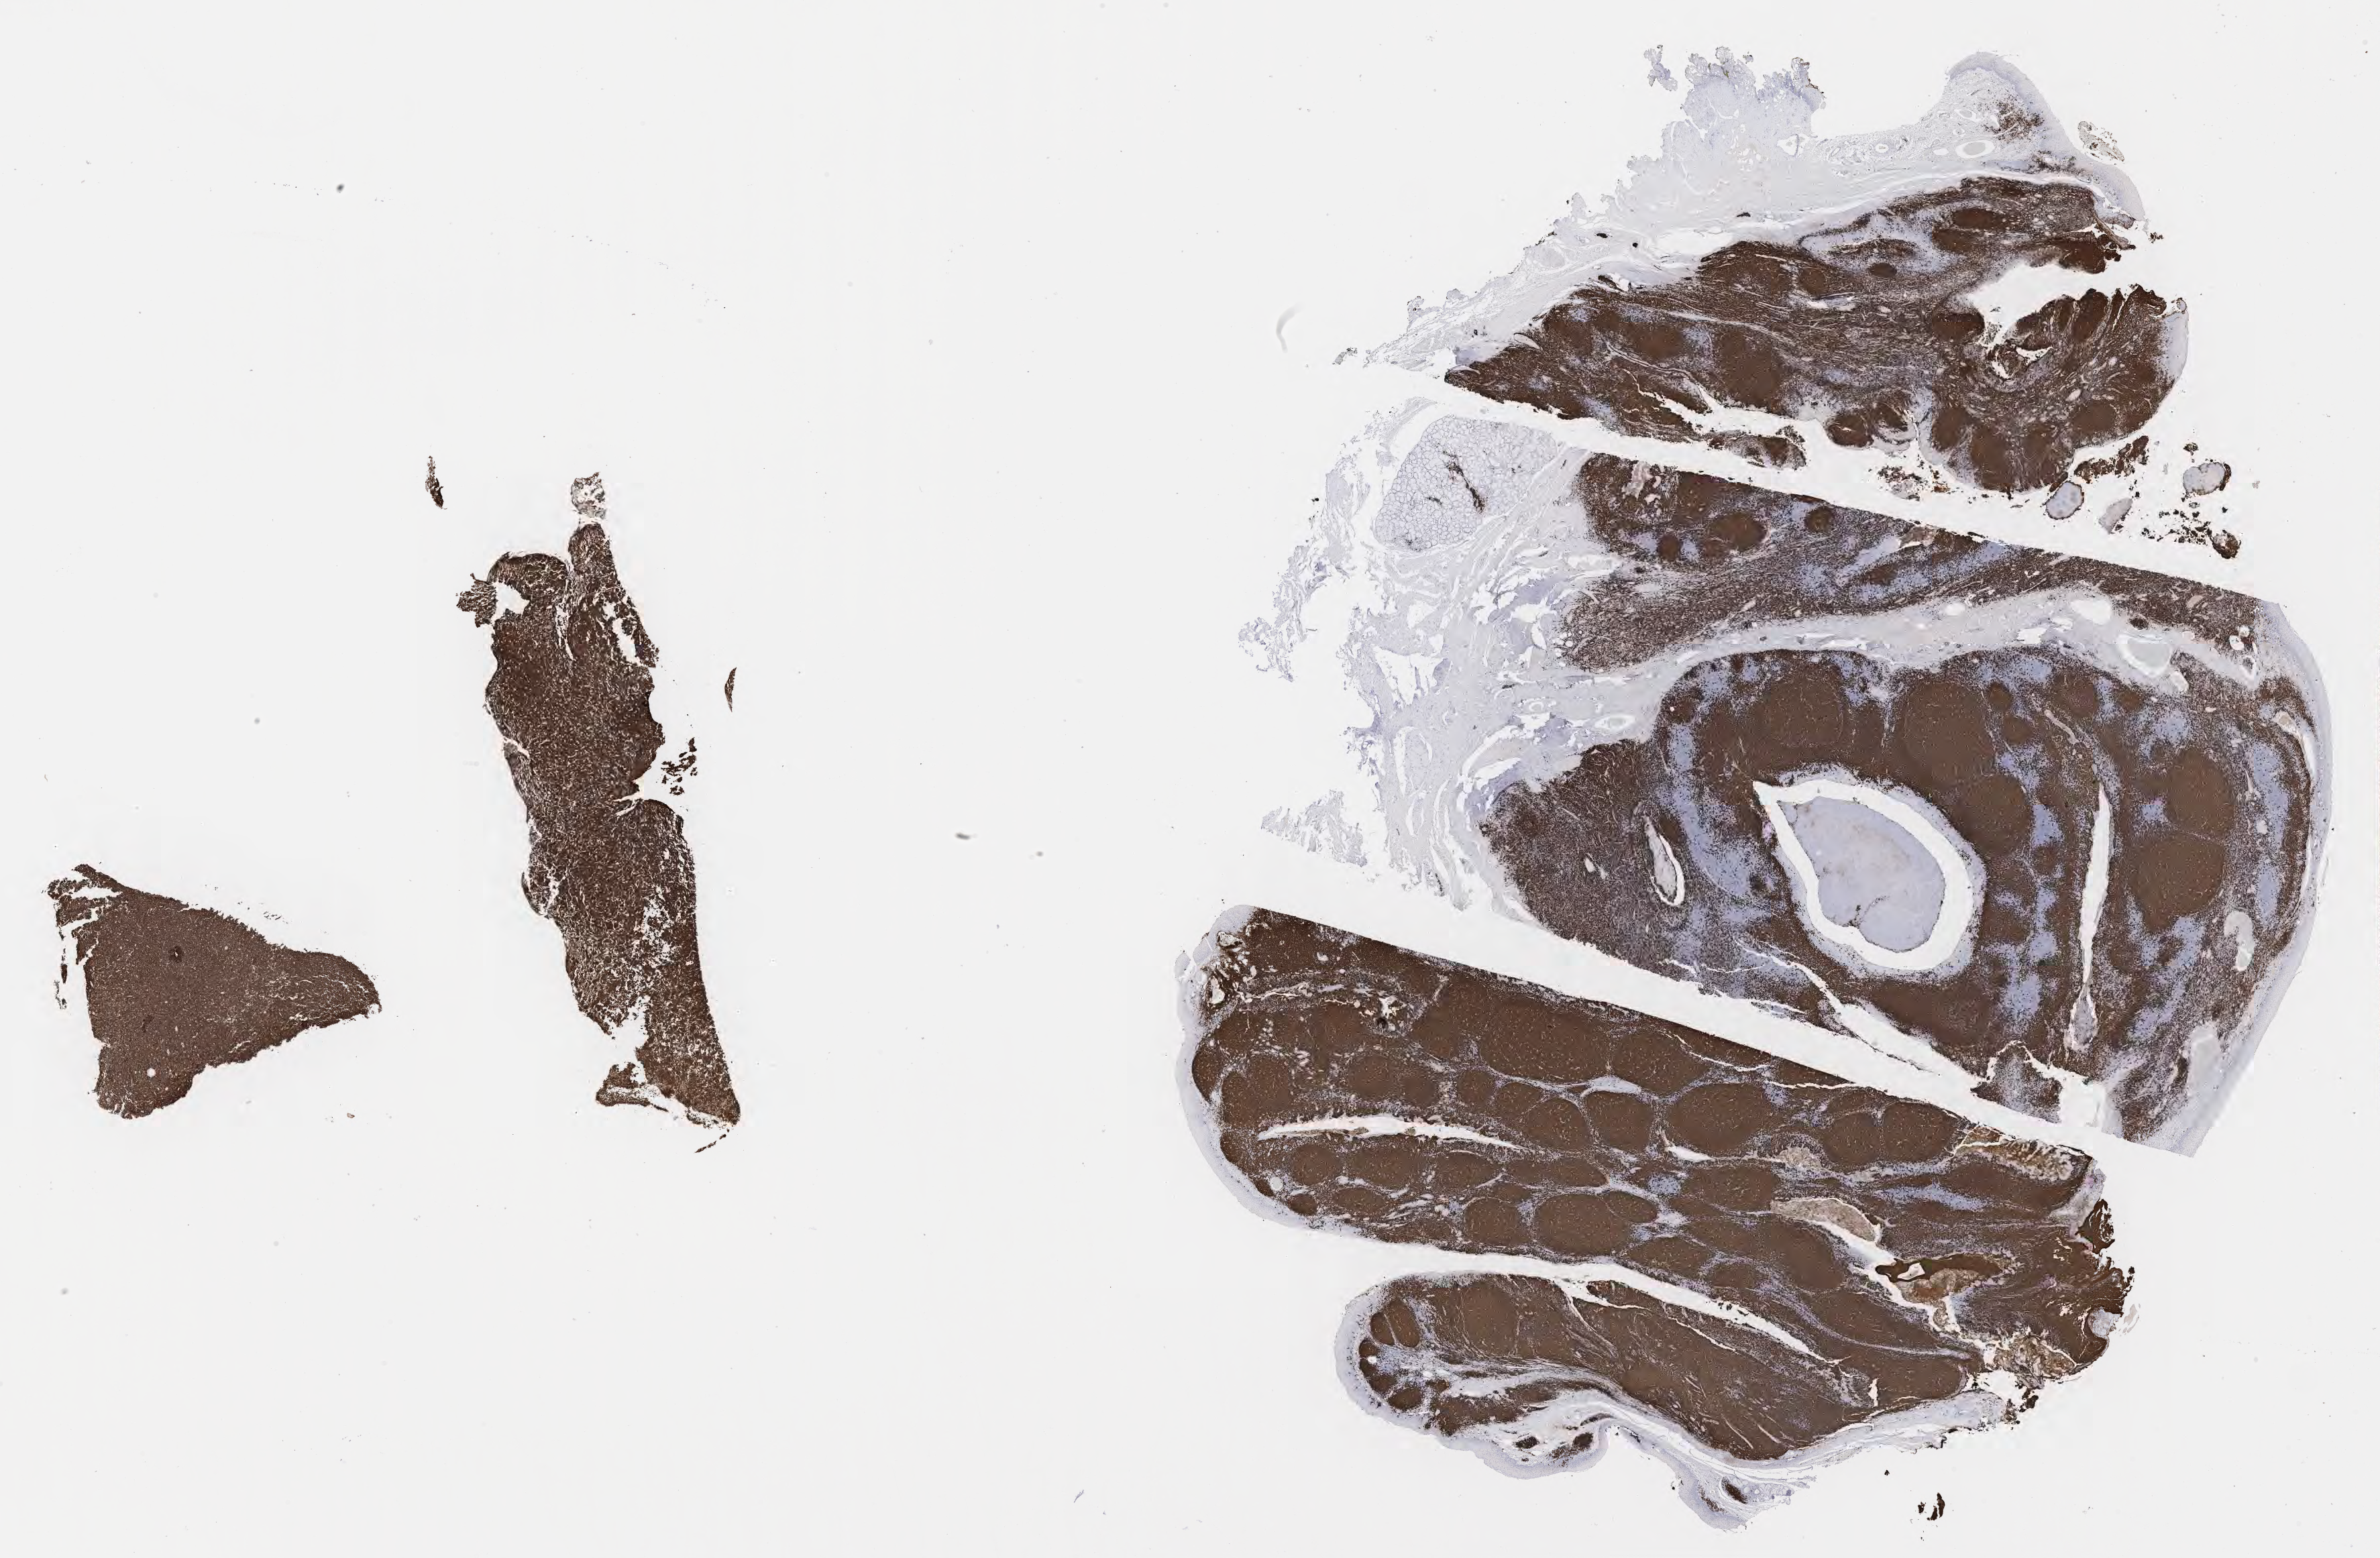
Whole-slide image, immunohistochemical stain for CD20, shown as a low-resolution overview of the whole scanned area (about 28.7 x 18.8 mm). Specimen: tumor tissue. Patient: male, age at initial diagnosis 2 years.
Diagnosis: Burkitt lymphoma, NOS.